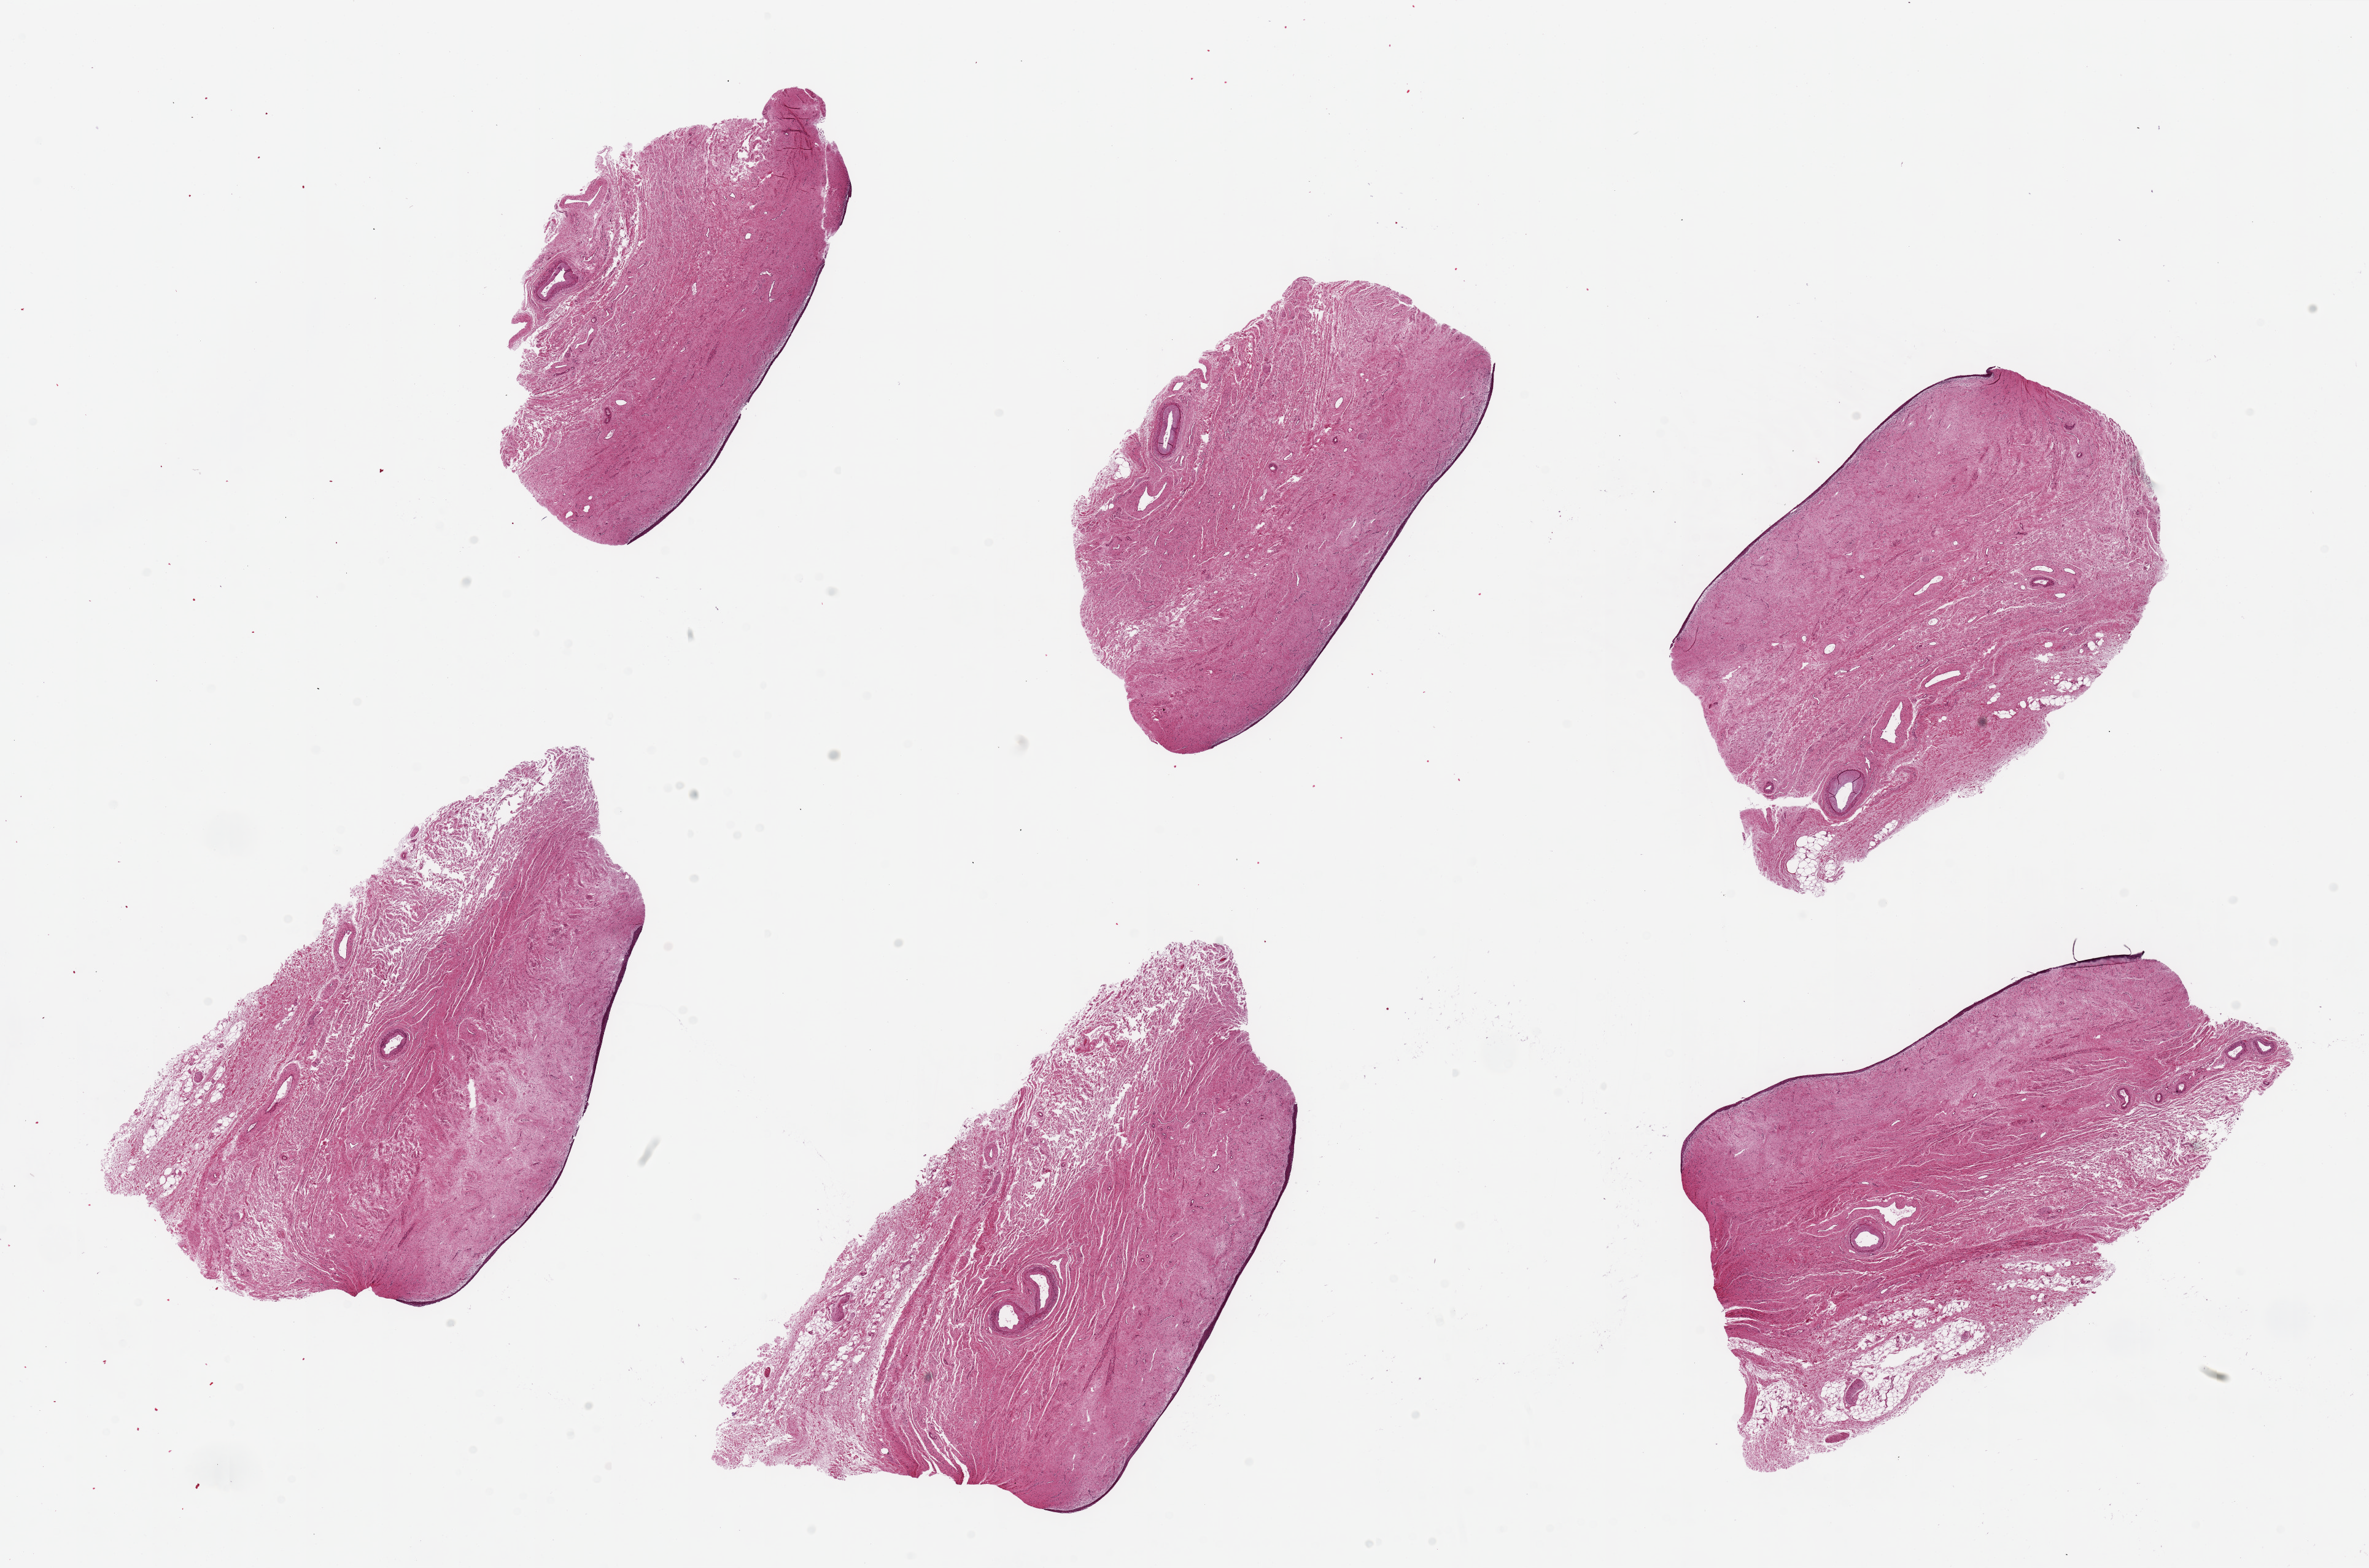
Whole-slide image, haematoxylin and eosin stain, brightfield — a low-resolution overview of the entire scanned area, about 30.5 x 20.2 mm; PAXgene-fixed, paraffin-embedded tissue; target tissue: vagina; donor tissue sample. Female donor.
Review note (as recorded): 6 pieces, up to 9x5mm; atrophic squamous mucosa is <1% thickness.